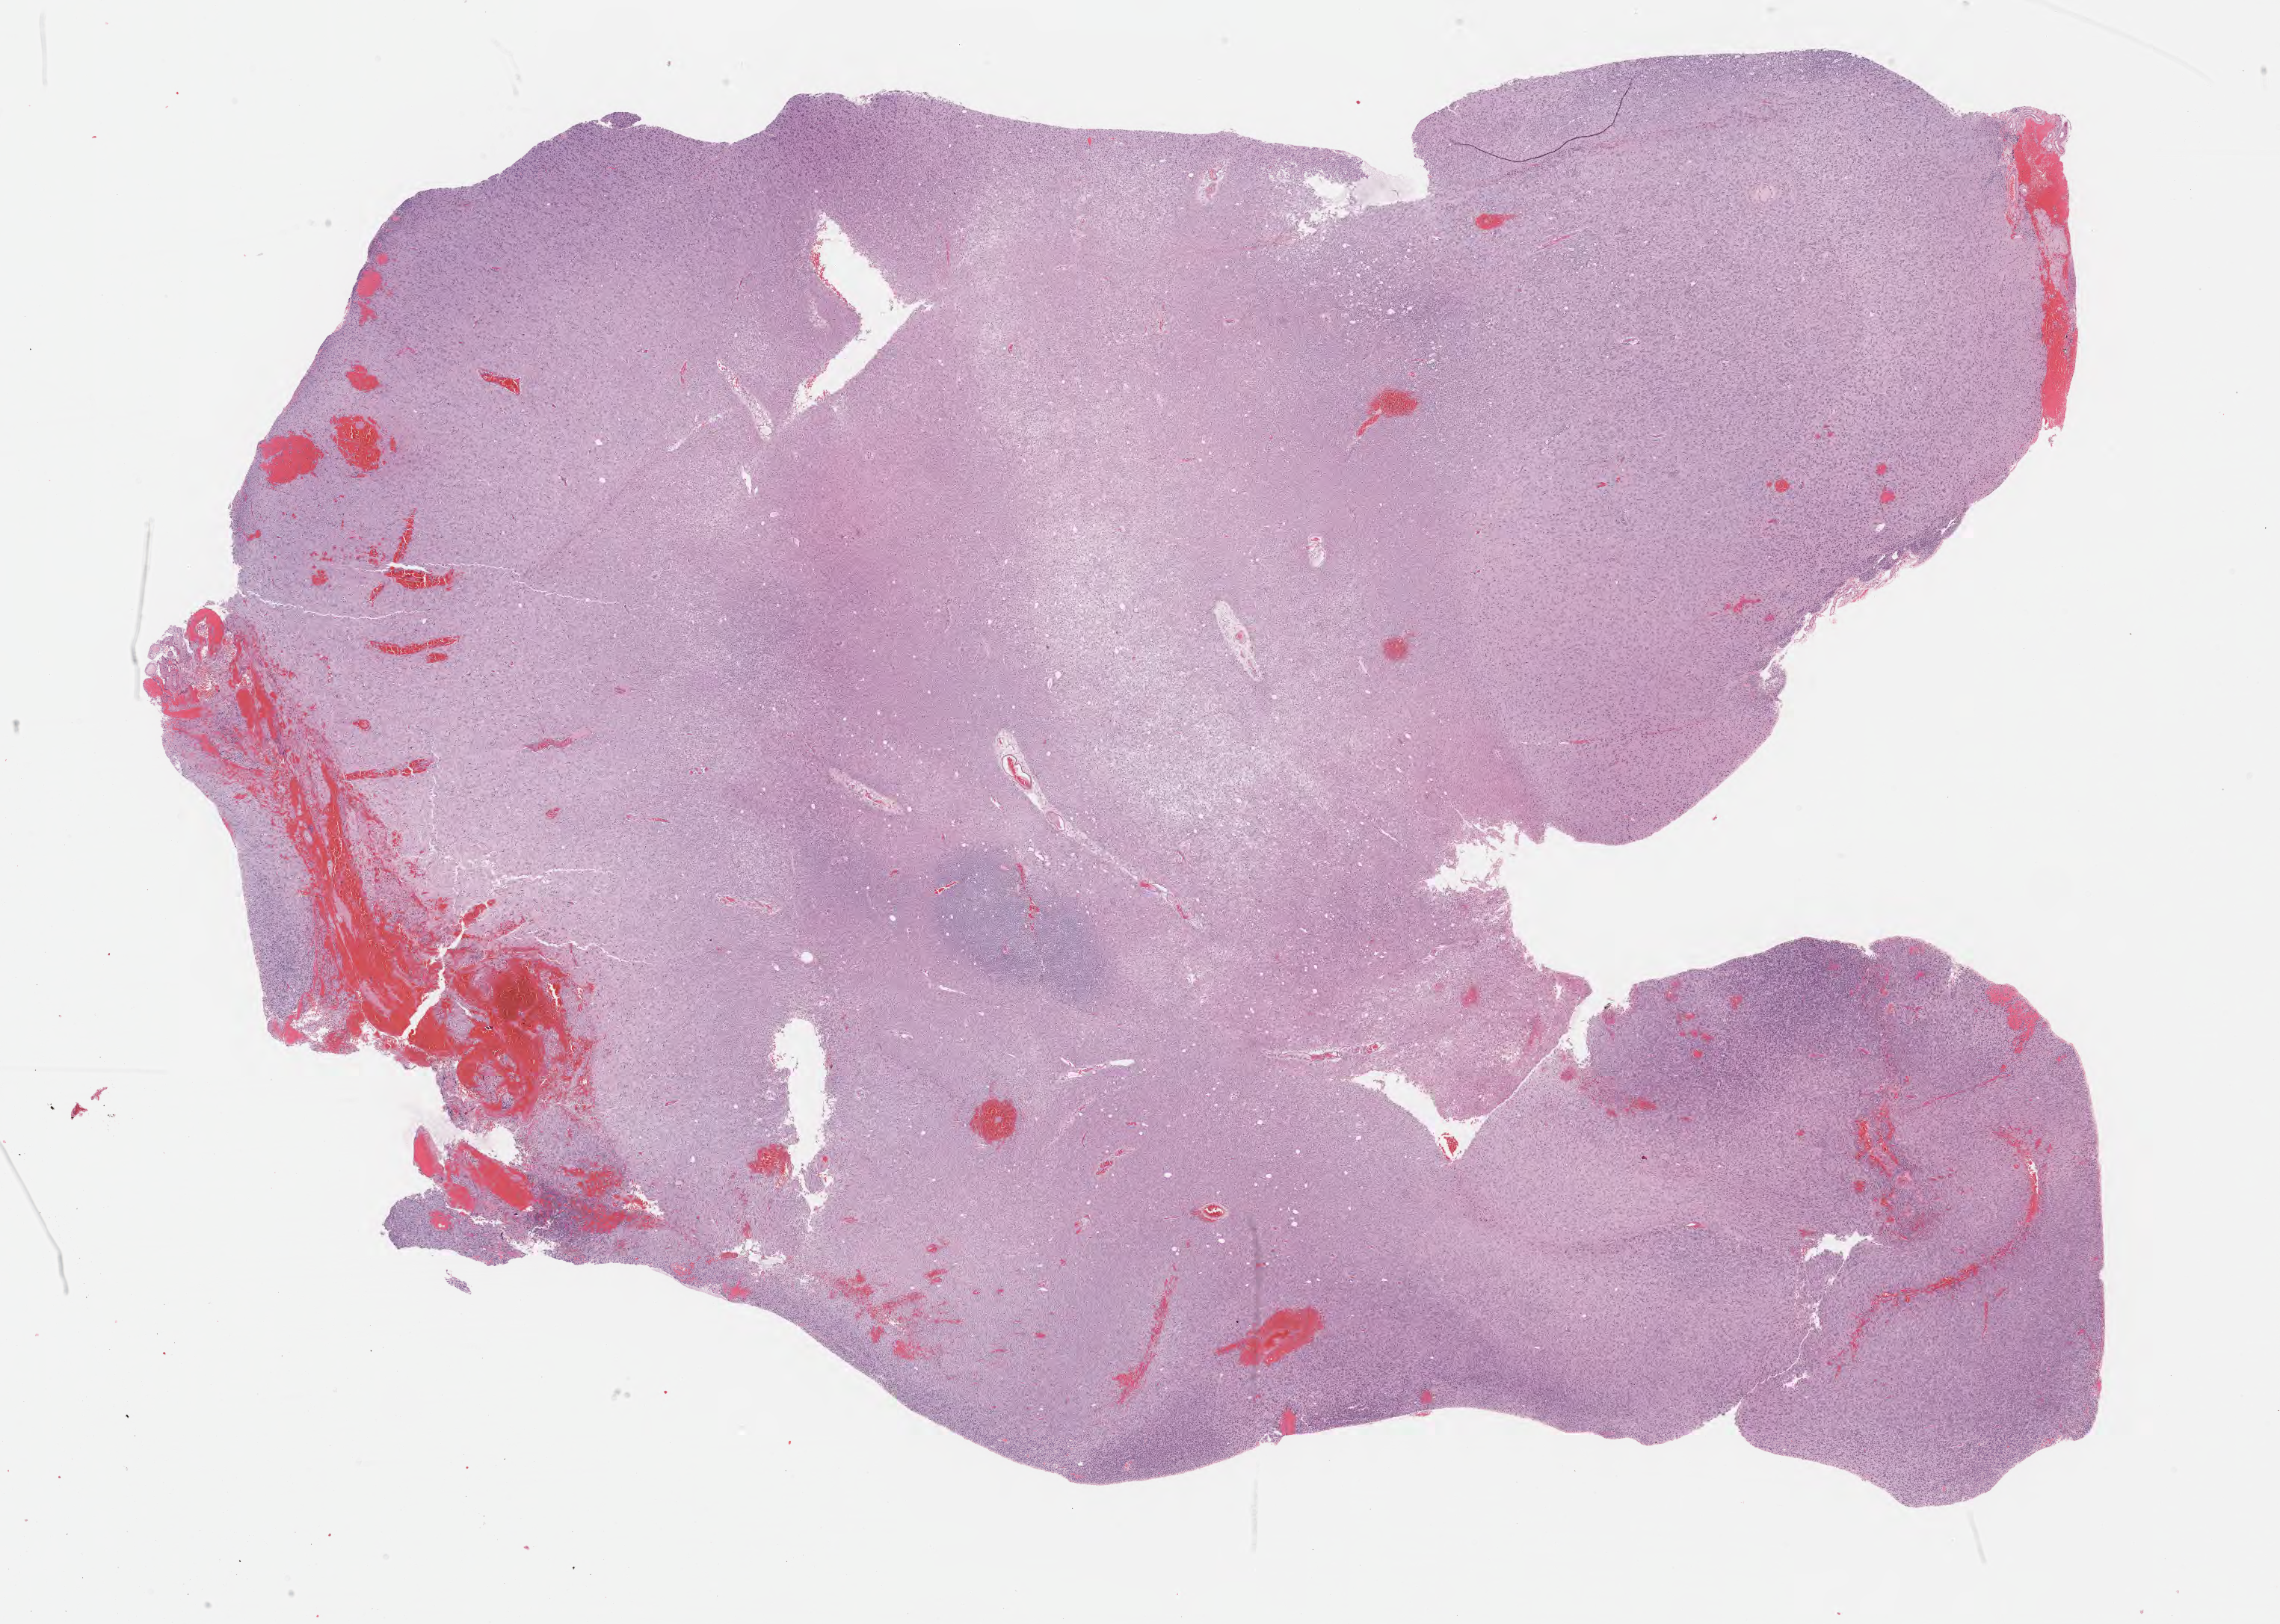
Digitized H&E-stained tissue section (whole slide) — whole scanned area (about 24.7 x 17.6 mm, acquisition: 40x scan) shown as a low-resolution overview.
Specimen: formalin-fixed paraffin-embedded (FFPE) diagnostic section; sample: primary tumour, brain.